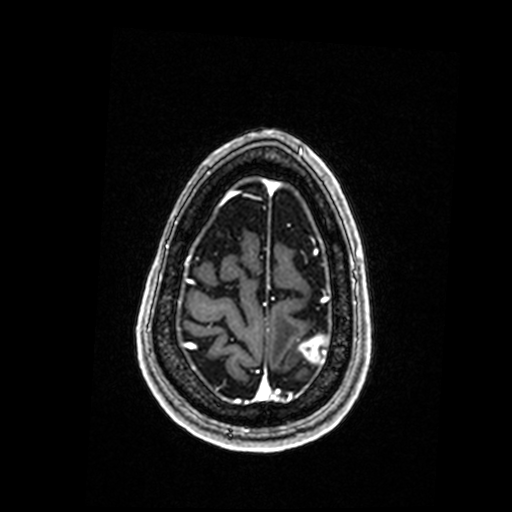
Brain MRI from a brain-tumour surgery series, one axial slice. Position 38 of 192 along the scan axis. T1-weighted post-contrast. 0.98 mm slice thickness. 512 × 512 image matrix. From the clinical record (not read from this slice): histopathology: Metastastic Carcinoma, Poorly Differentiated.
Annotated regions visible in this slice (manually delineated by an expert):
- tumour: bounding box <300,336,329,364> (left, top, right, bottom; pixels)